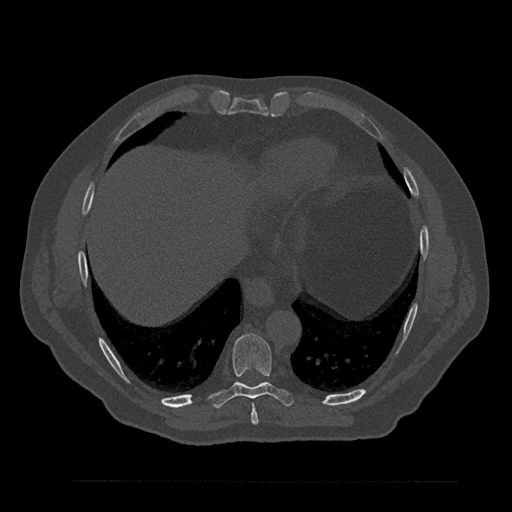
CT including the spine, one axial slice; position 407 of 797 along the scan axis; bone window (W 1800 / L 400 HU); 0.5 mm slice thickness; 512 × 512 image matrix, field of view 430 × 430 mm. Male patient, age 61 years. Case-level facts recorded for this patient, not image findings: primary cancer: prostate.
Structures marked on this image (semi-automatic segmentation, software-assisted and operator-edited):
- T8 vertebra: box from (x=251, y=404) to (x=259, y=425) px
- T9 vertebra: (x=209, y=334)–(x=294, y=408)